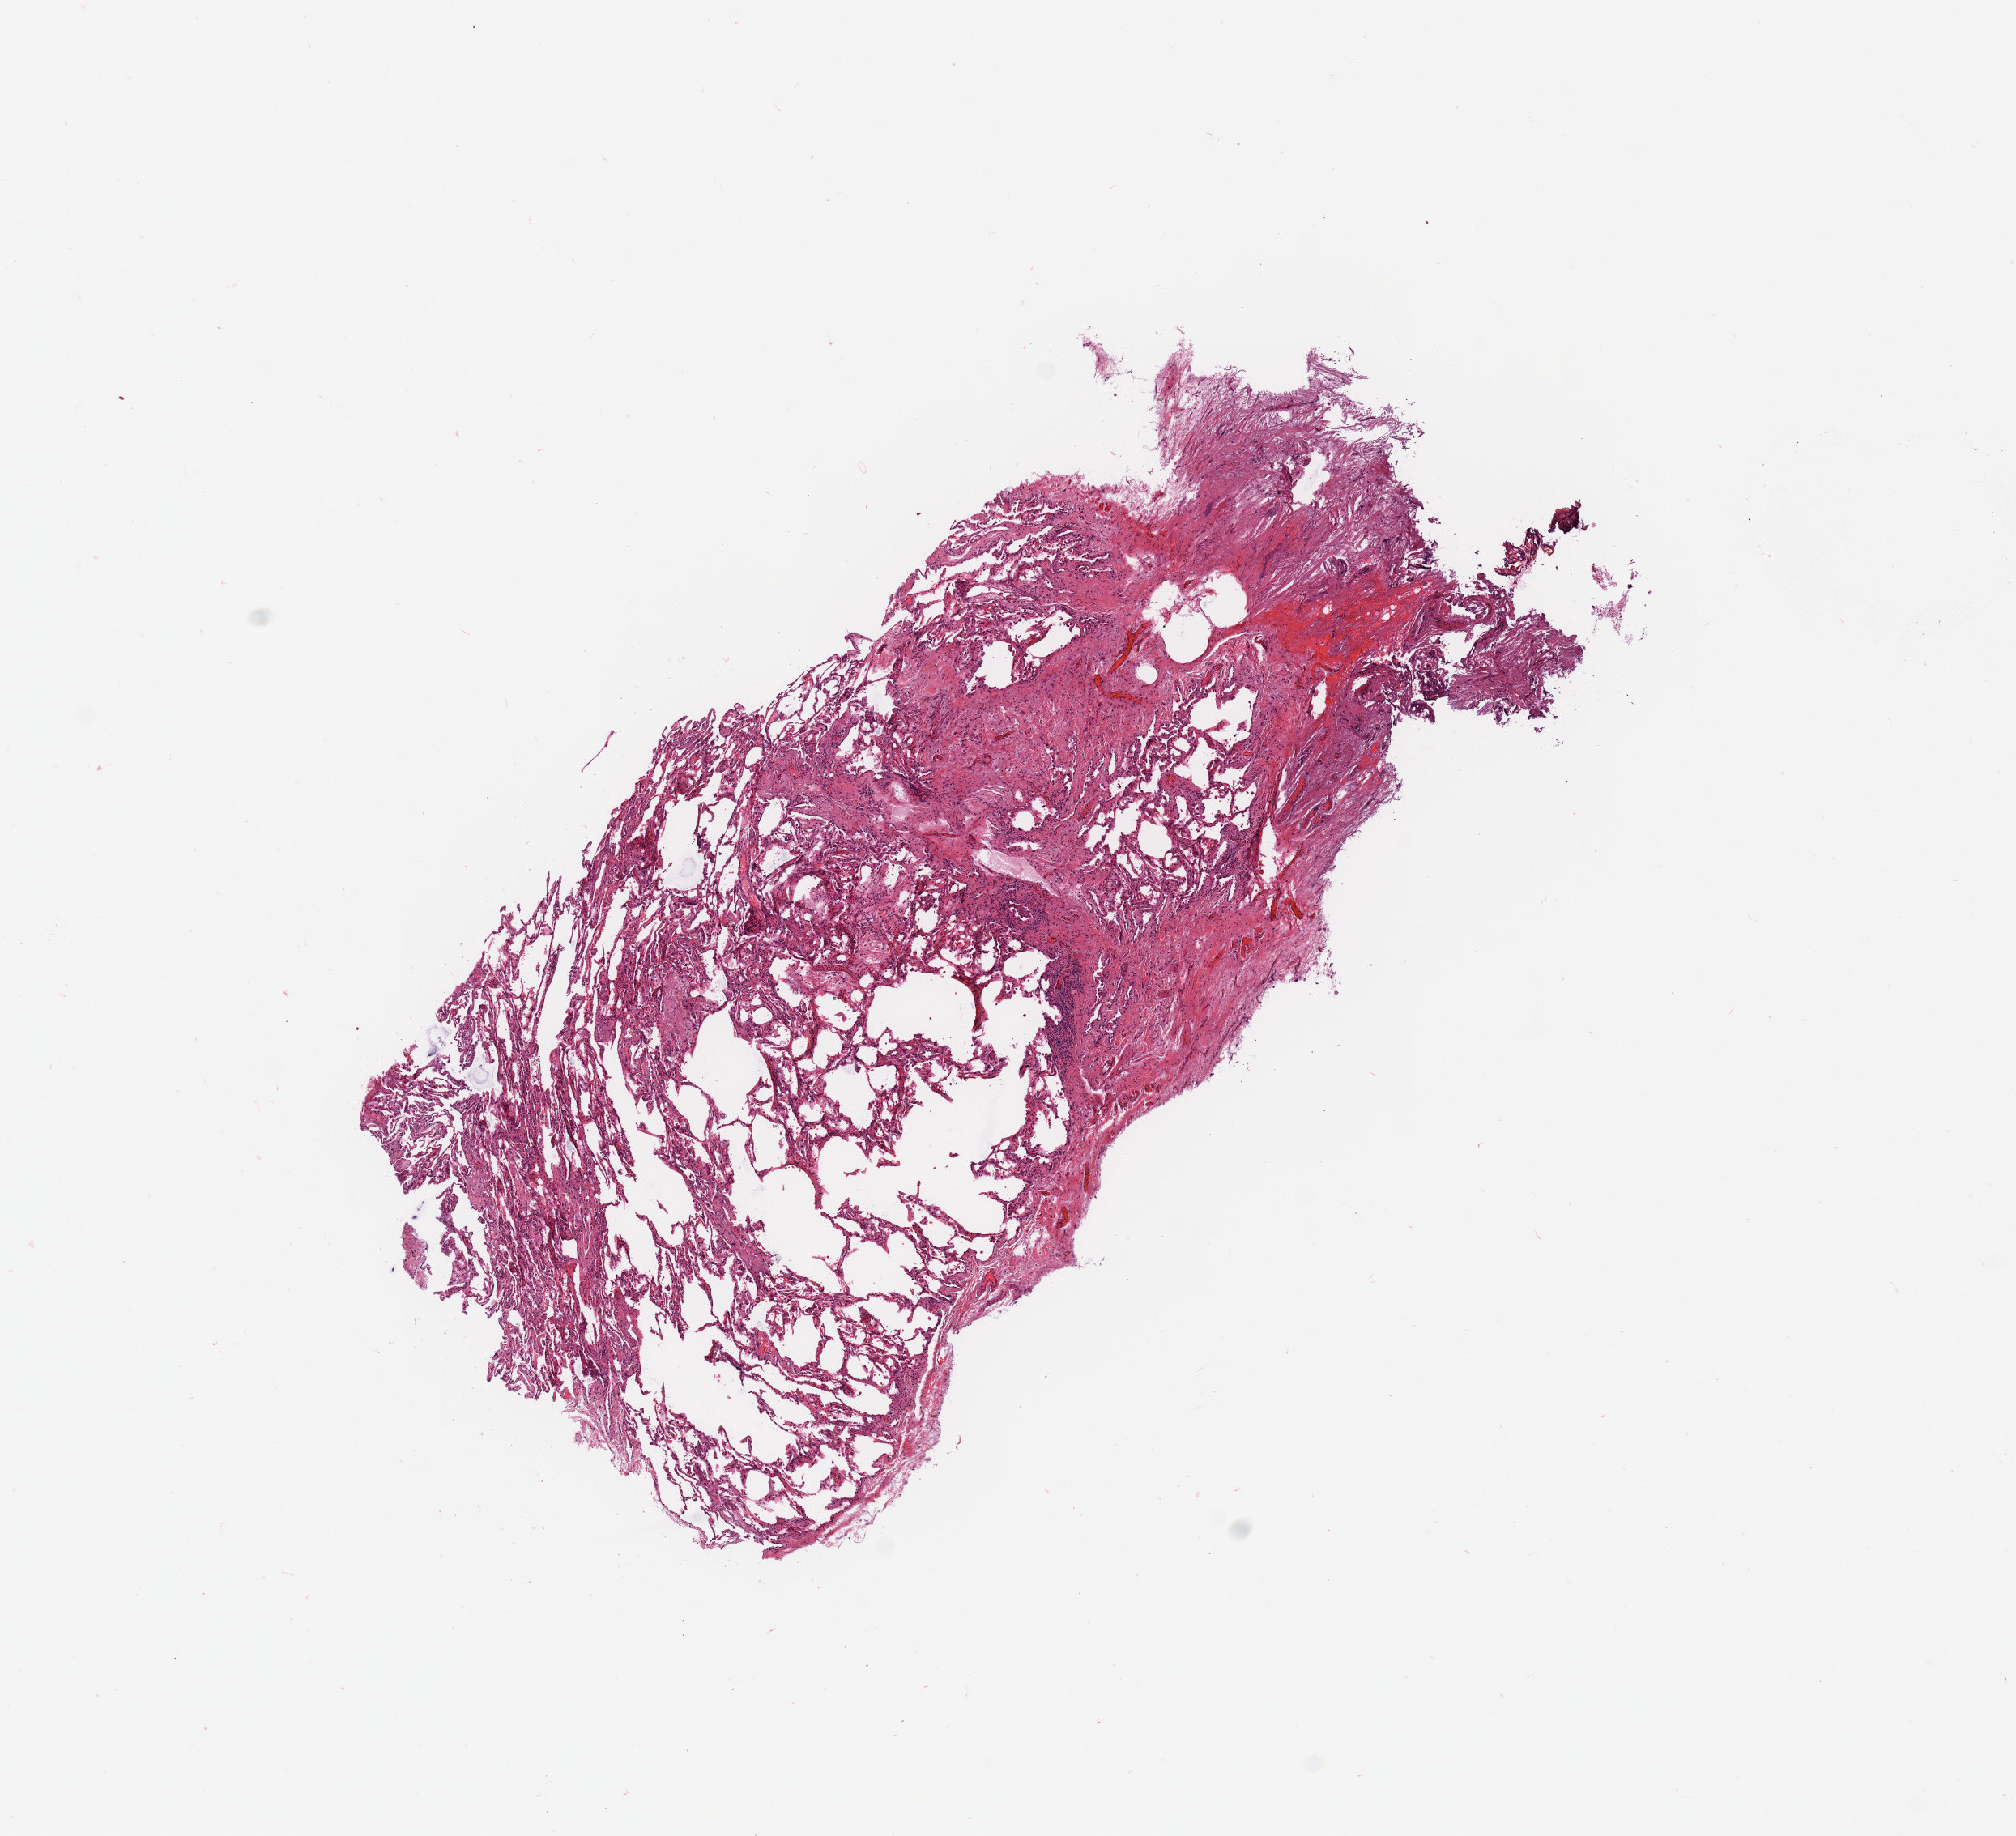
Digitized H&E tissue section (whole slide) — shown as a low-resolution overview of the whole scanned area (about 9.8 x 9.0 mm), normal (non-tumour) tissue sample, lung. 67-year-old male patient.
This section: normal (non-tumour) tissue from the same patient. Patient diagnosis: Squamous cell carcinoma, NOS.